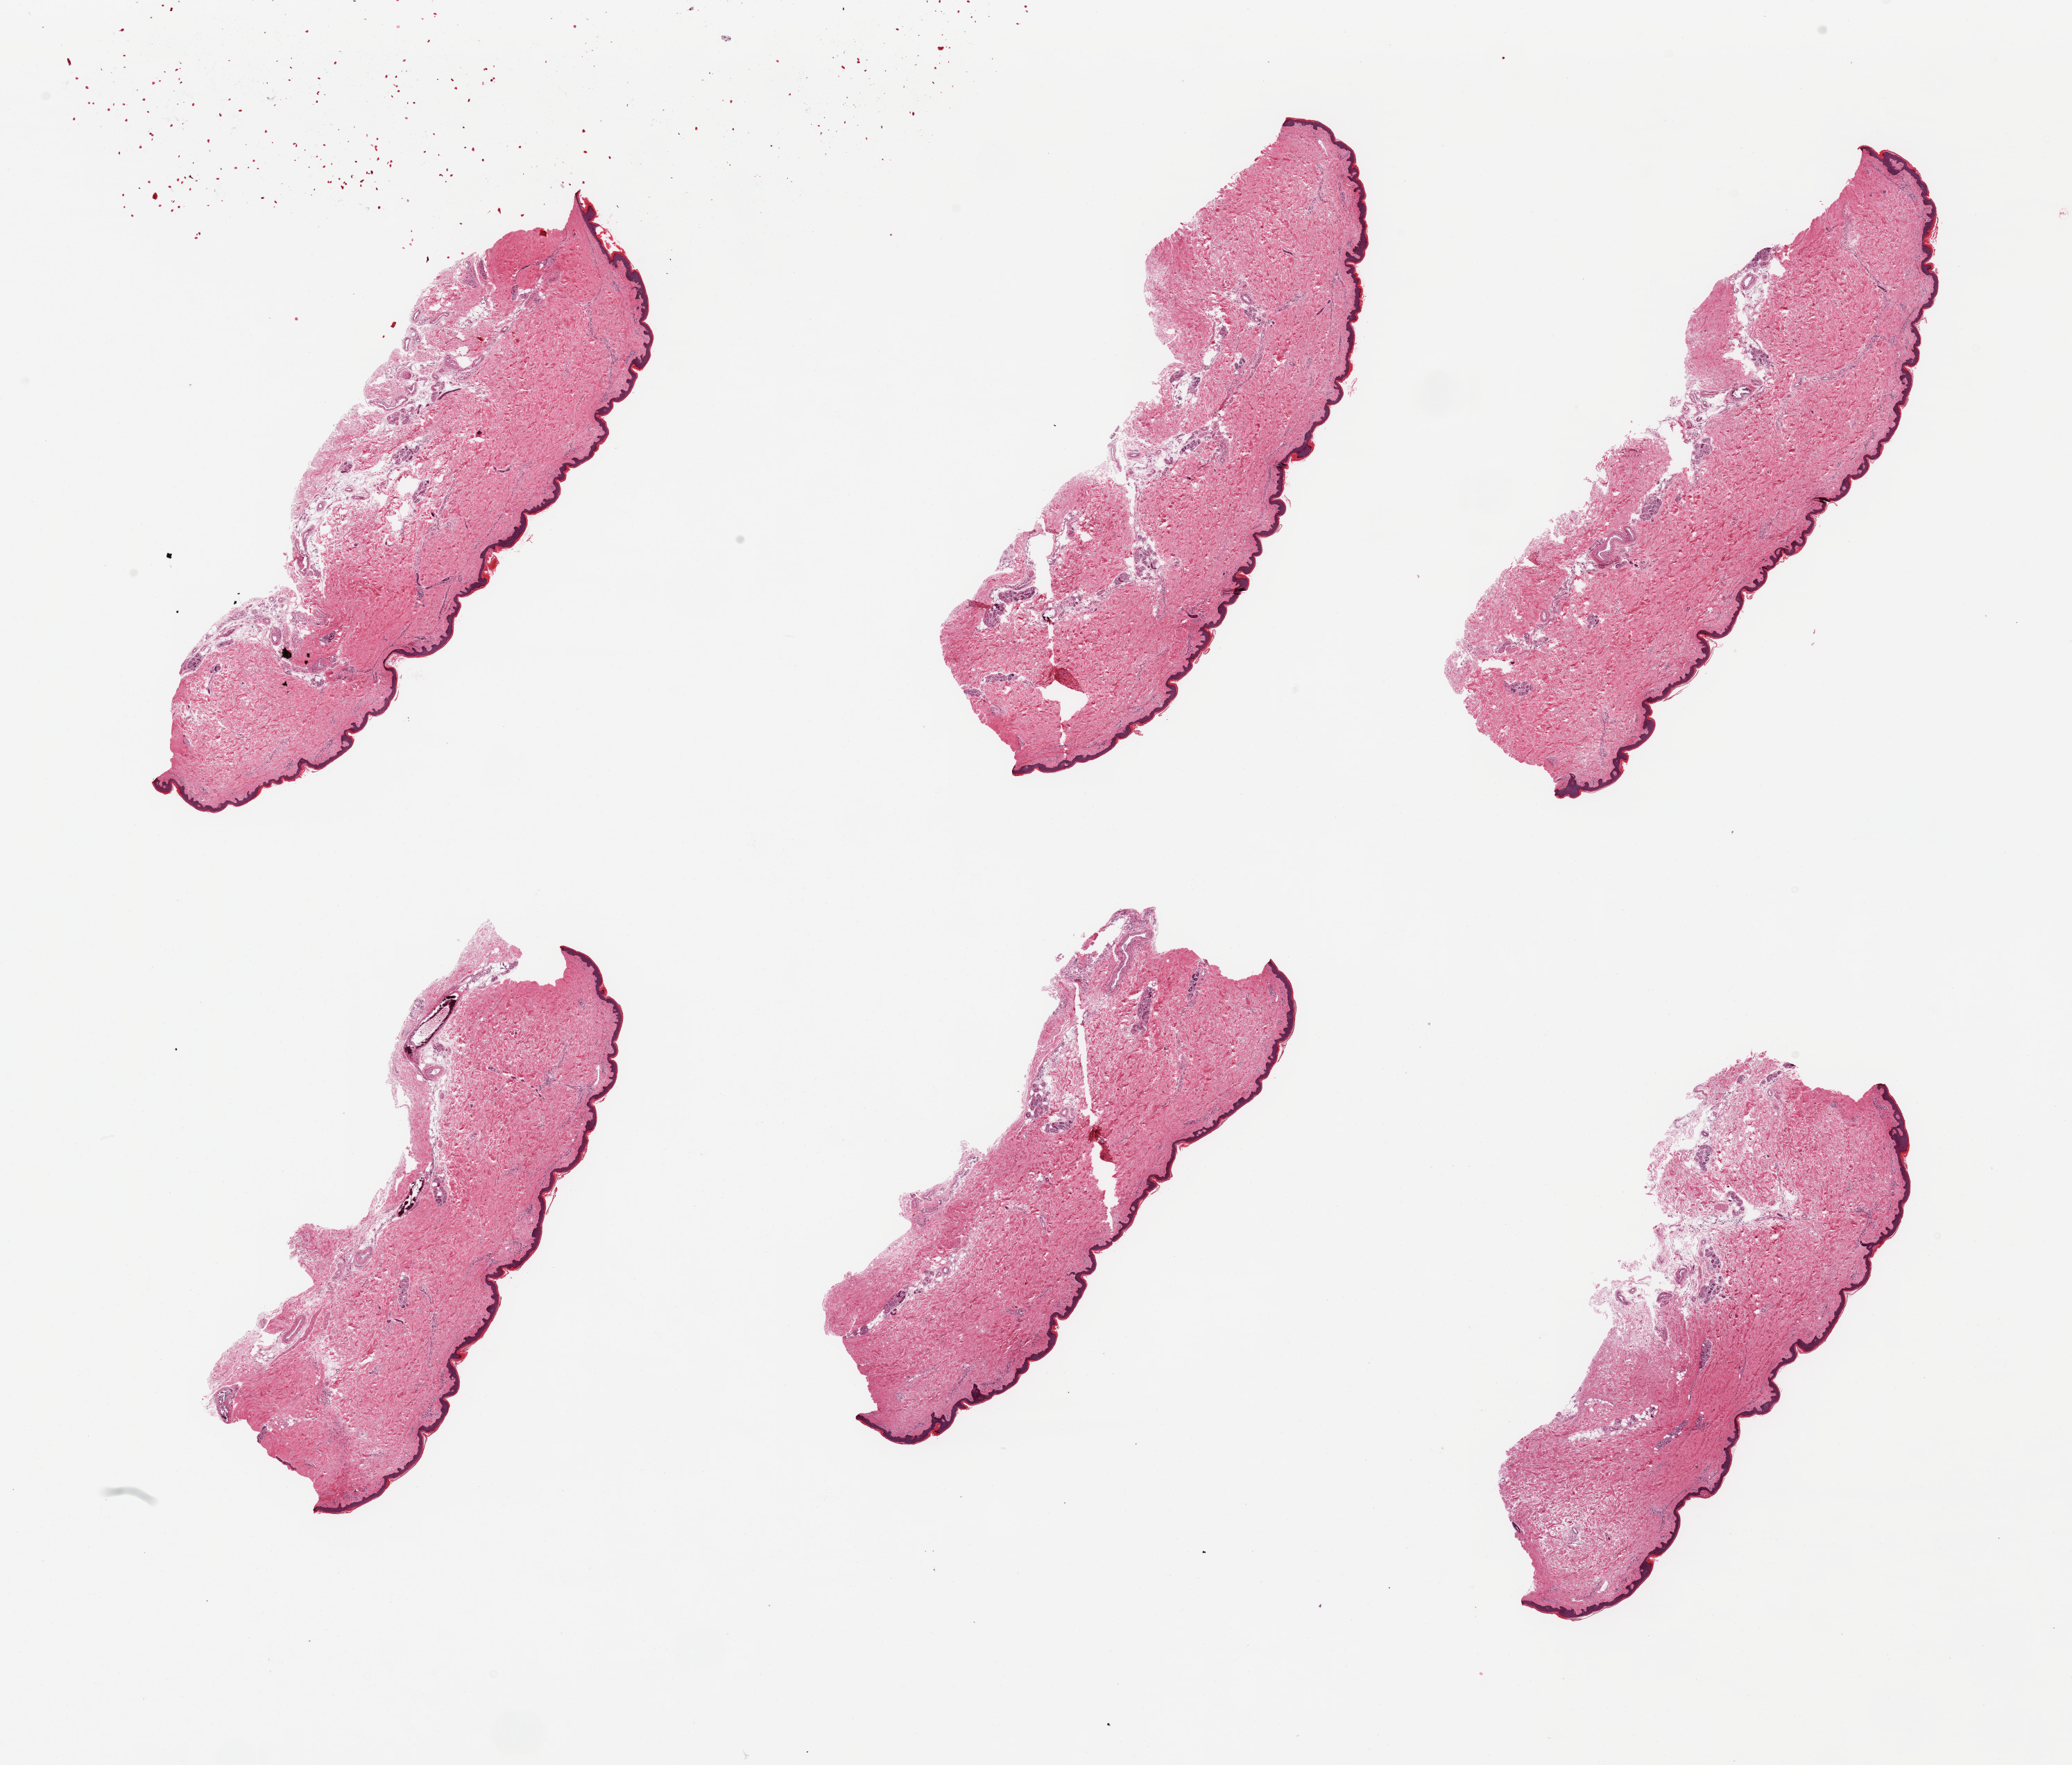
Whole-slide image, hematoxylin and eosin (H&E) stain, whole scanned area (about 23.6 x 20.1 mm, from a 20x scan) shown as a low-resolution overview, PAXgene-fixed paraffin-embedded (PFPE) section, section of skin of lower leg (target tissue), donor tissue sample. Donor sex: female.
Review note (as recorded): 2 pieces, minimal dermal fat; squamous epithelium is ~50 microns.